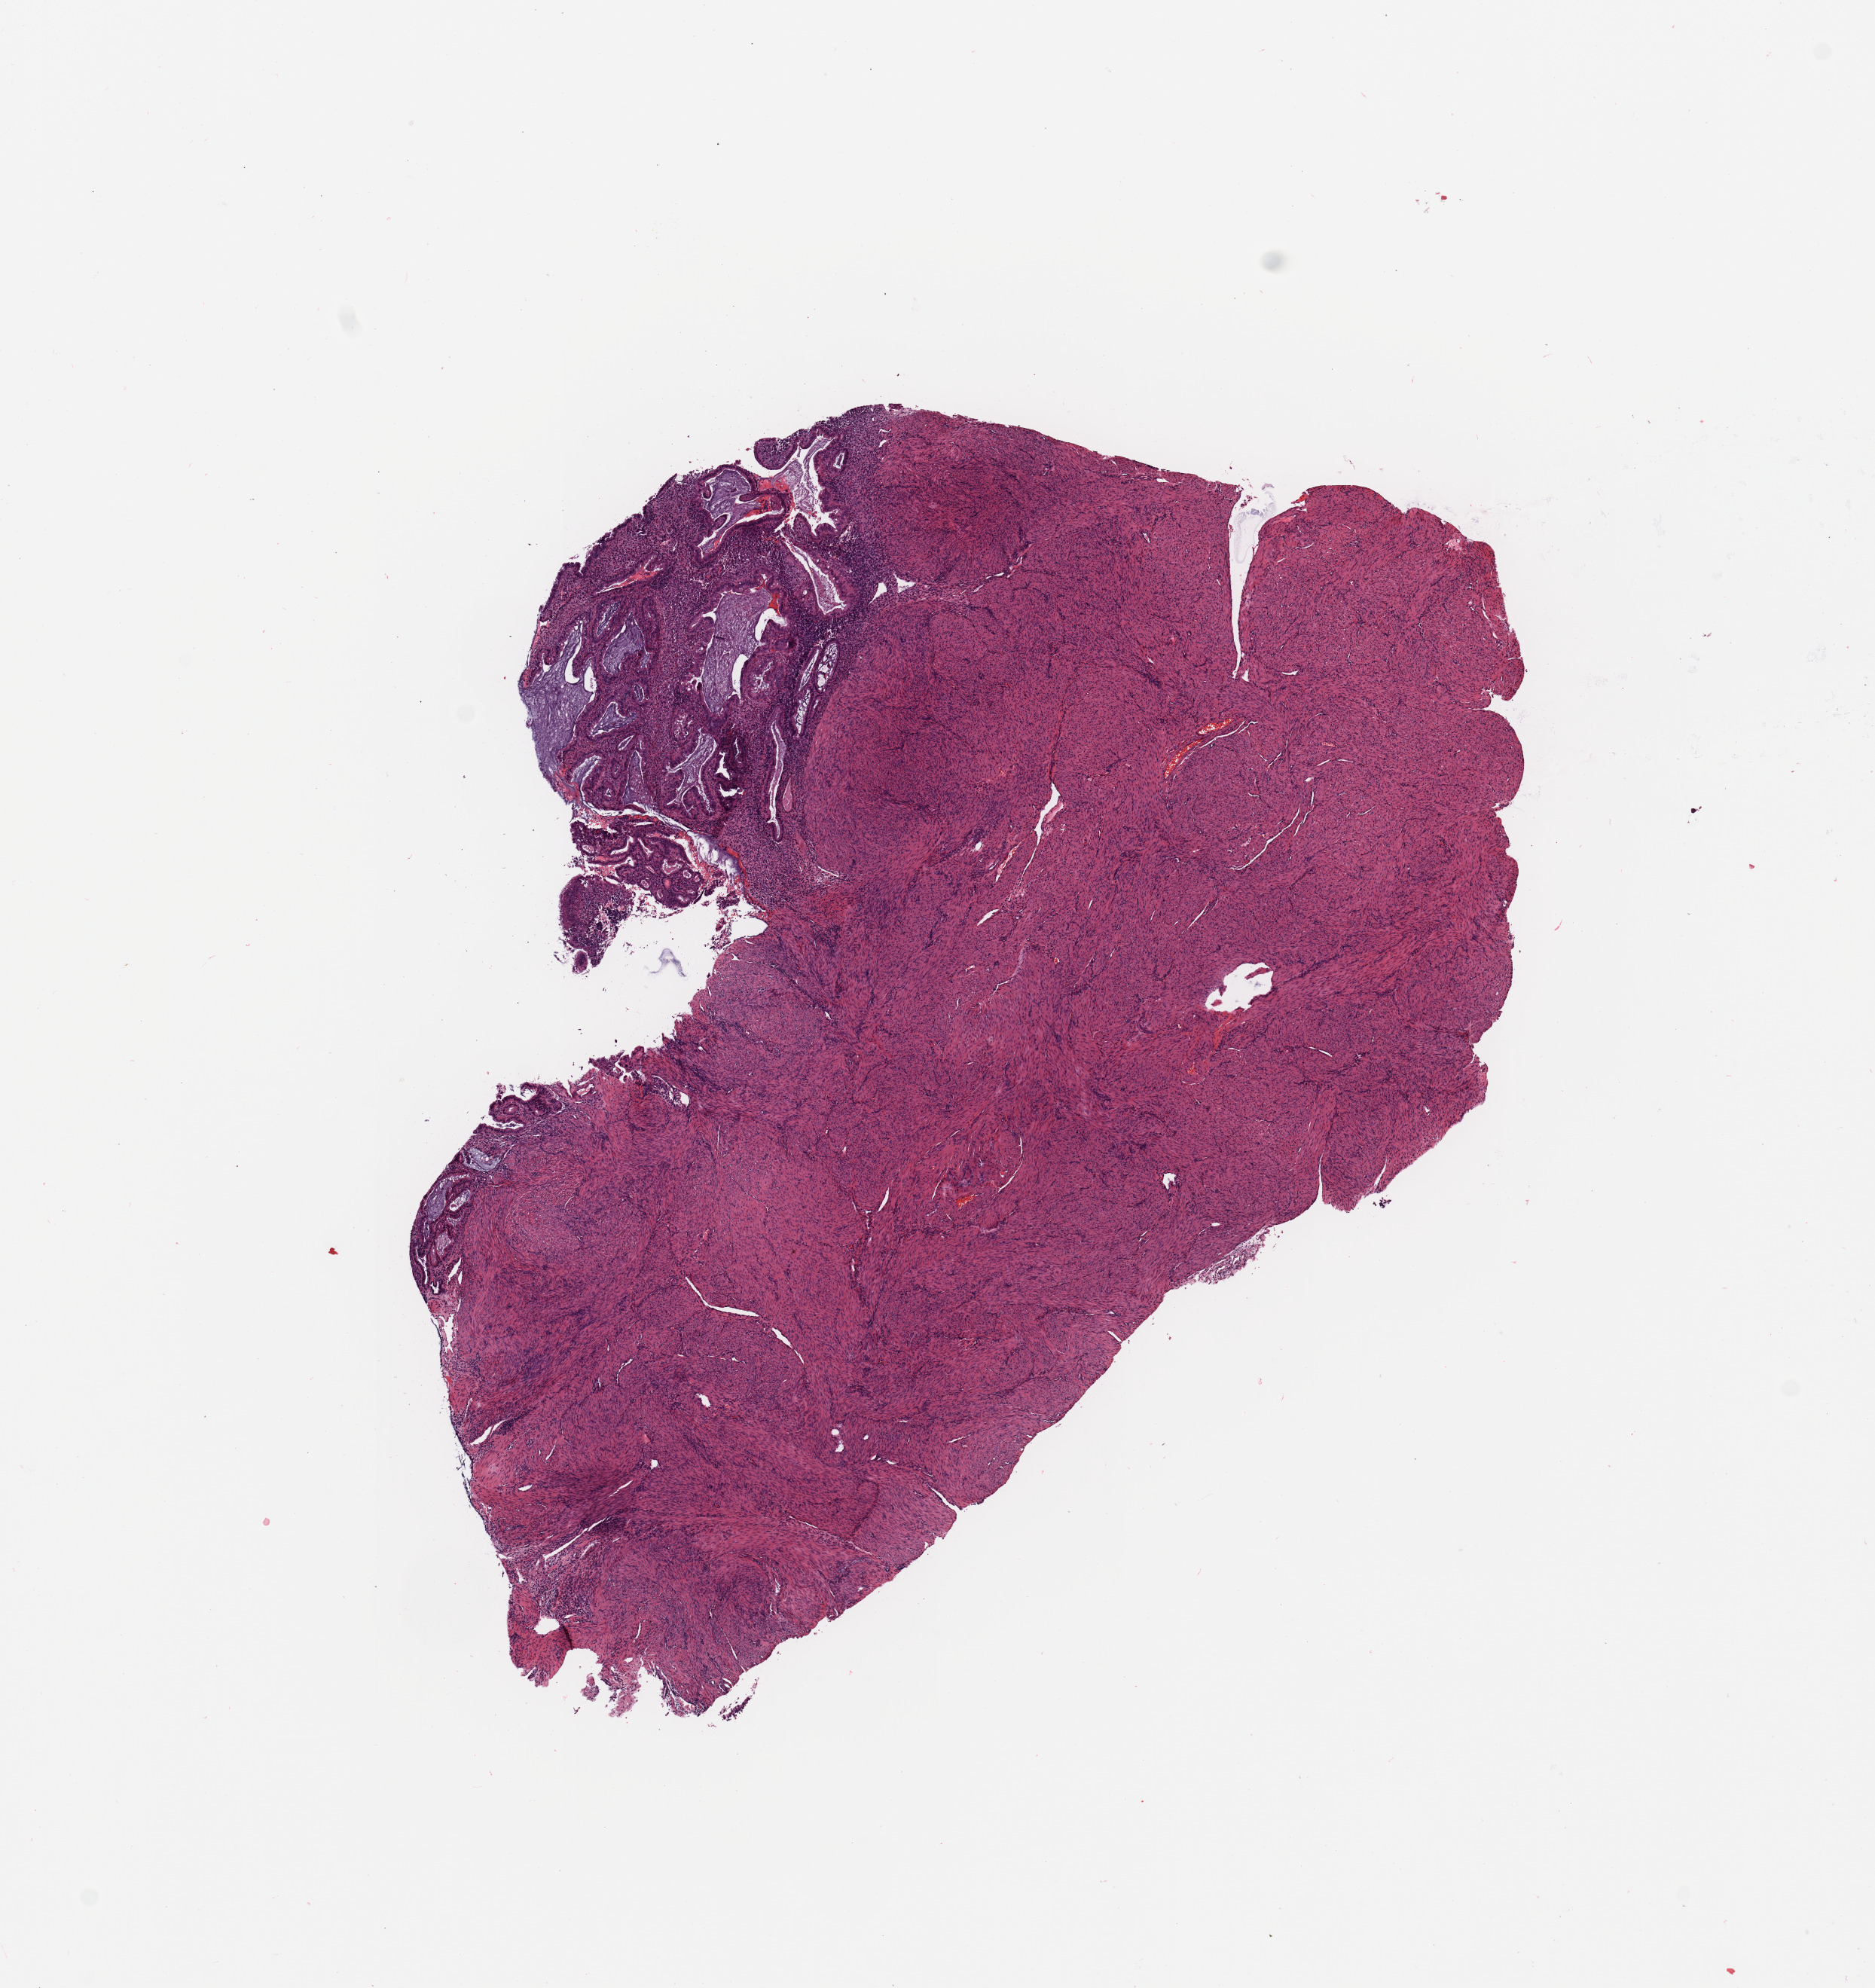
Whole-slide histology image, H&E — shown as a low-resolution overview of the whole scanned area (about 9.8 x 10.4 mm, acquisition: 20x scan); tumour tissue sample, uterus. Female, 63 y/o. Histologic grade: G1 (well differentiated).
• AJCC pathologic stage: I
• histologic diagnosis: Endometrioid adenocarcinoma, NOS